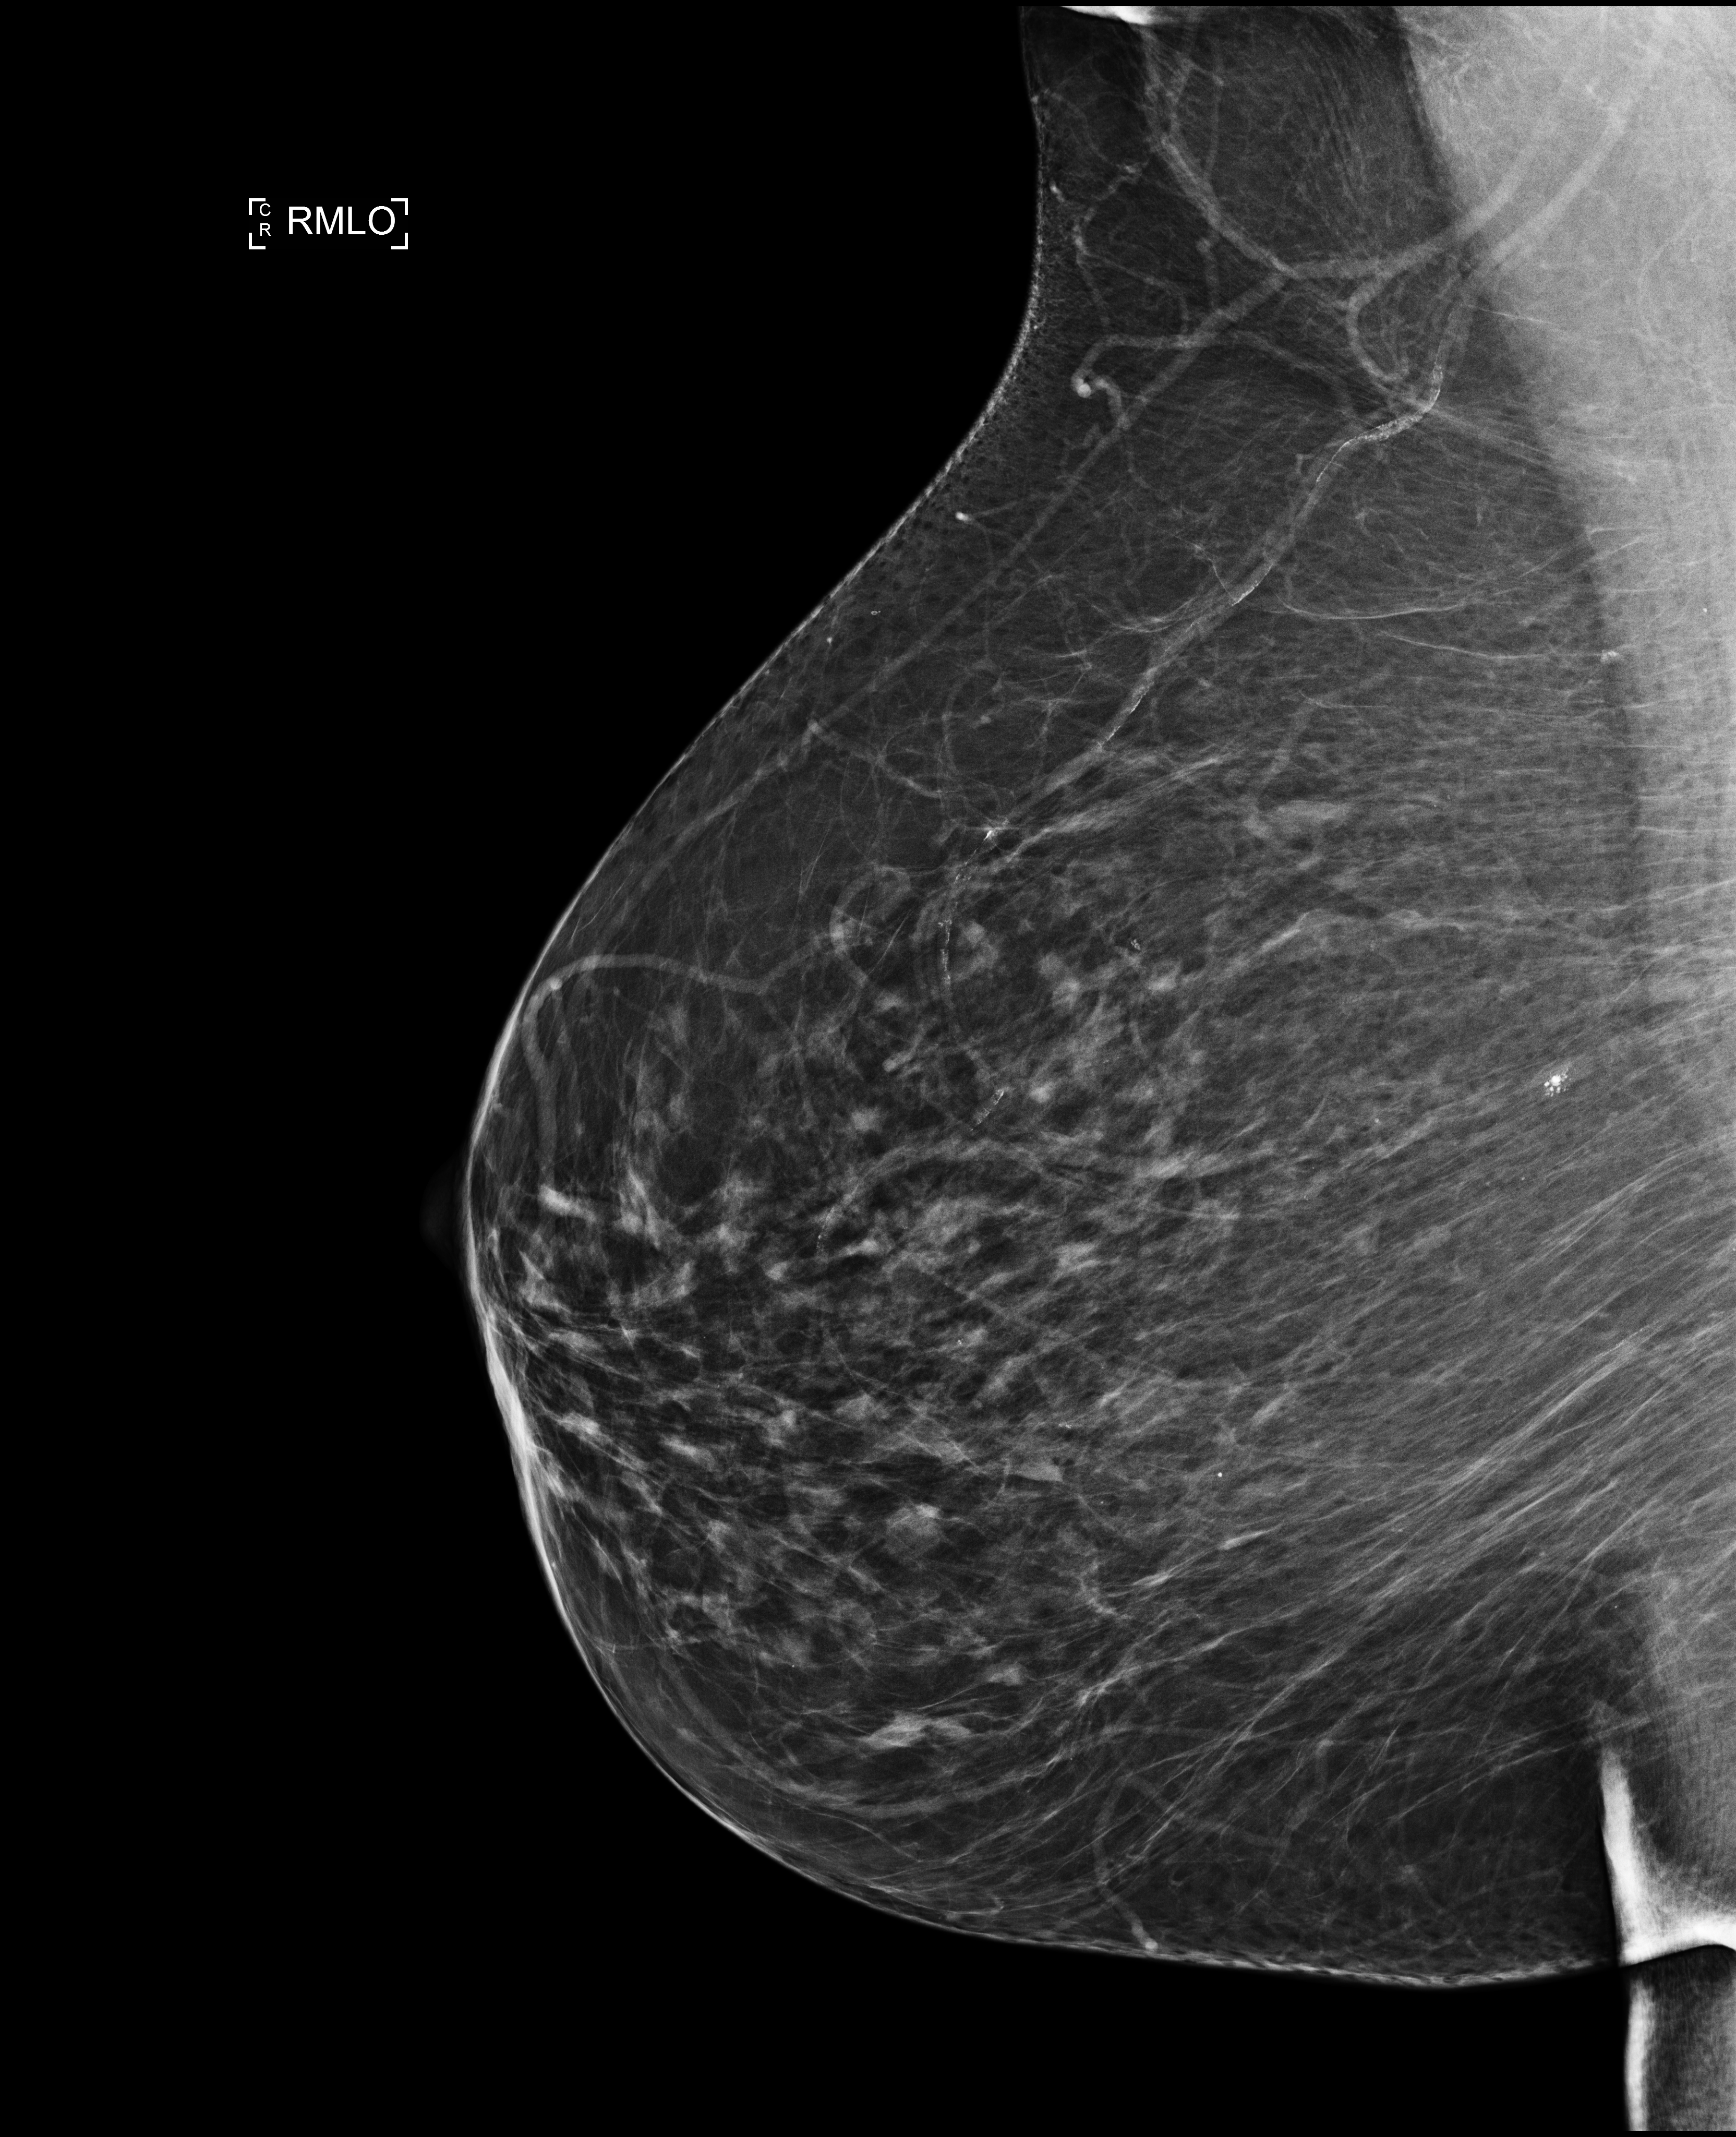
Annual screening mammography examination, compressed breast thickness 74 mm, system: Selenia Dimensions. Patient aged 74 years (female).
Image type: full-field digital mammogram. Breast: right. Projection: MLO view.